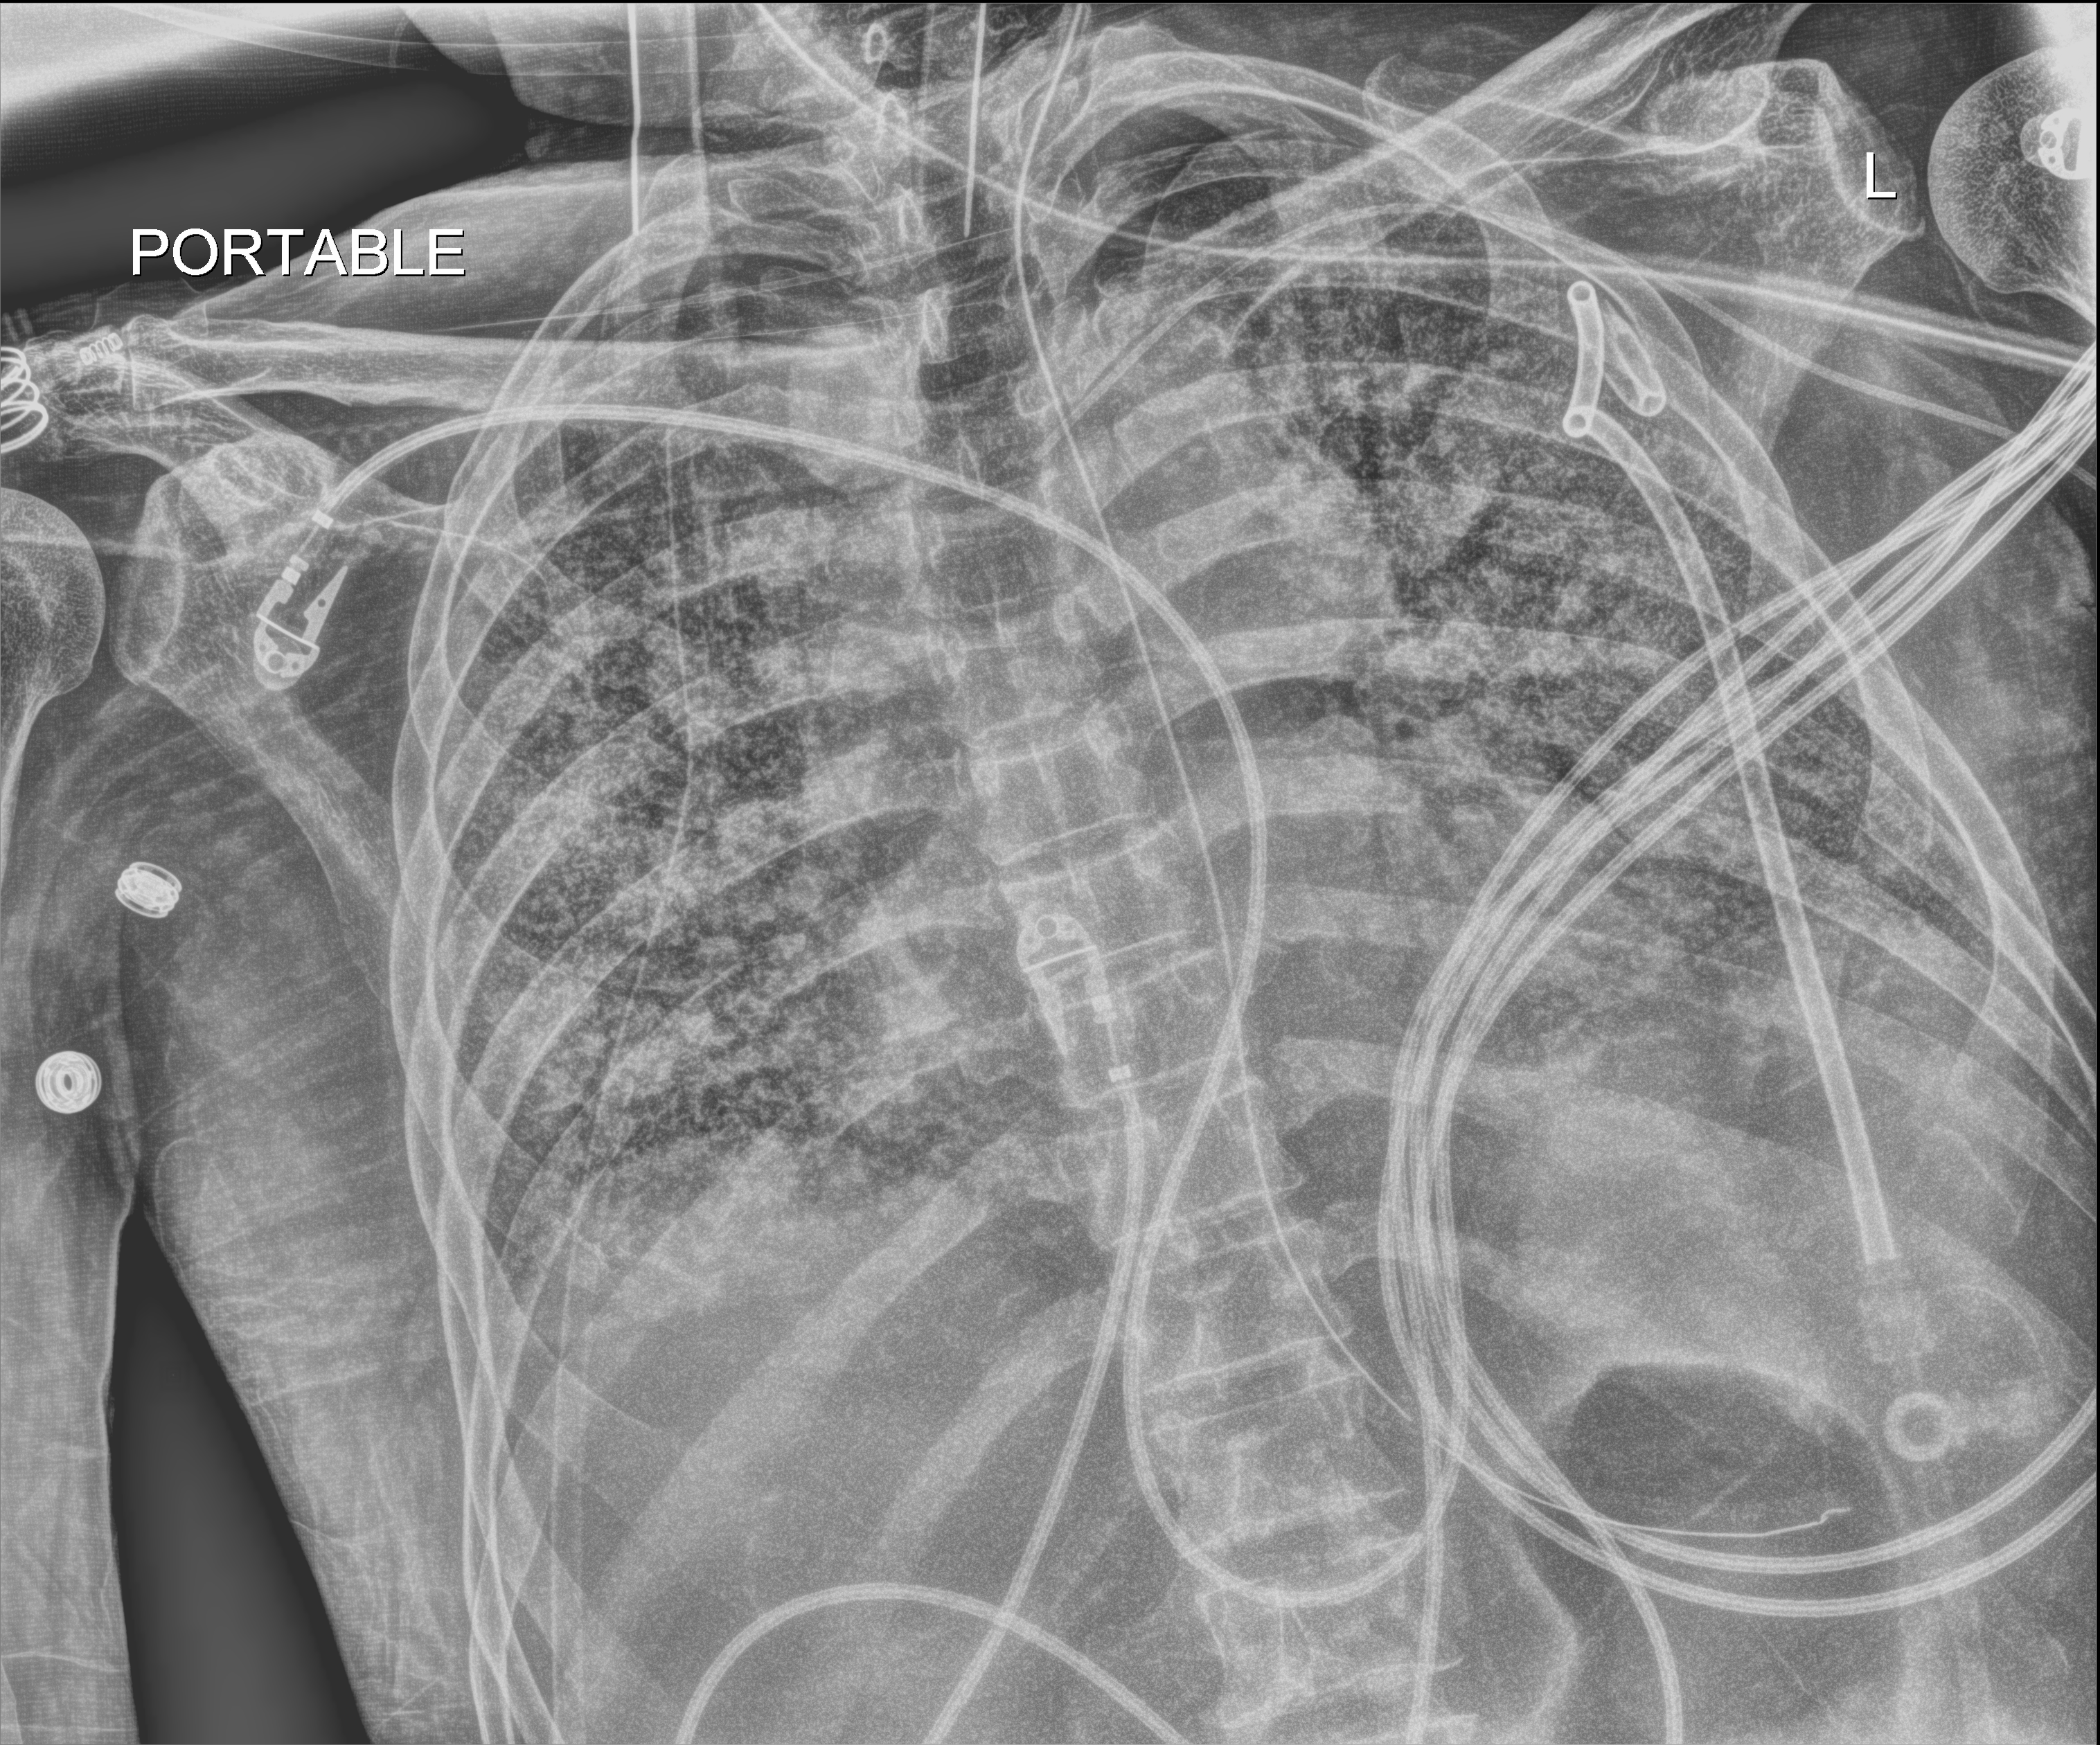
Chest X-ray (portable). Male patient hospitalised with COVID-19, age 60–74 years.
From the hospital-stay record, not from the radiograph (when in the stay this image was taken is not recorded): length of hospital stay: 54 days.